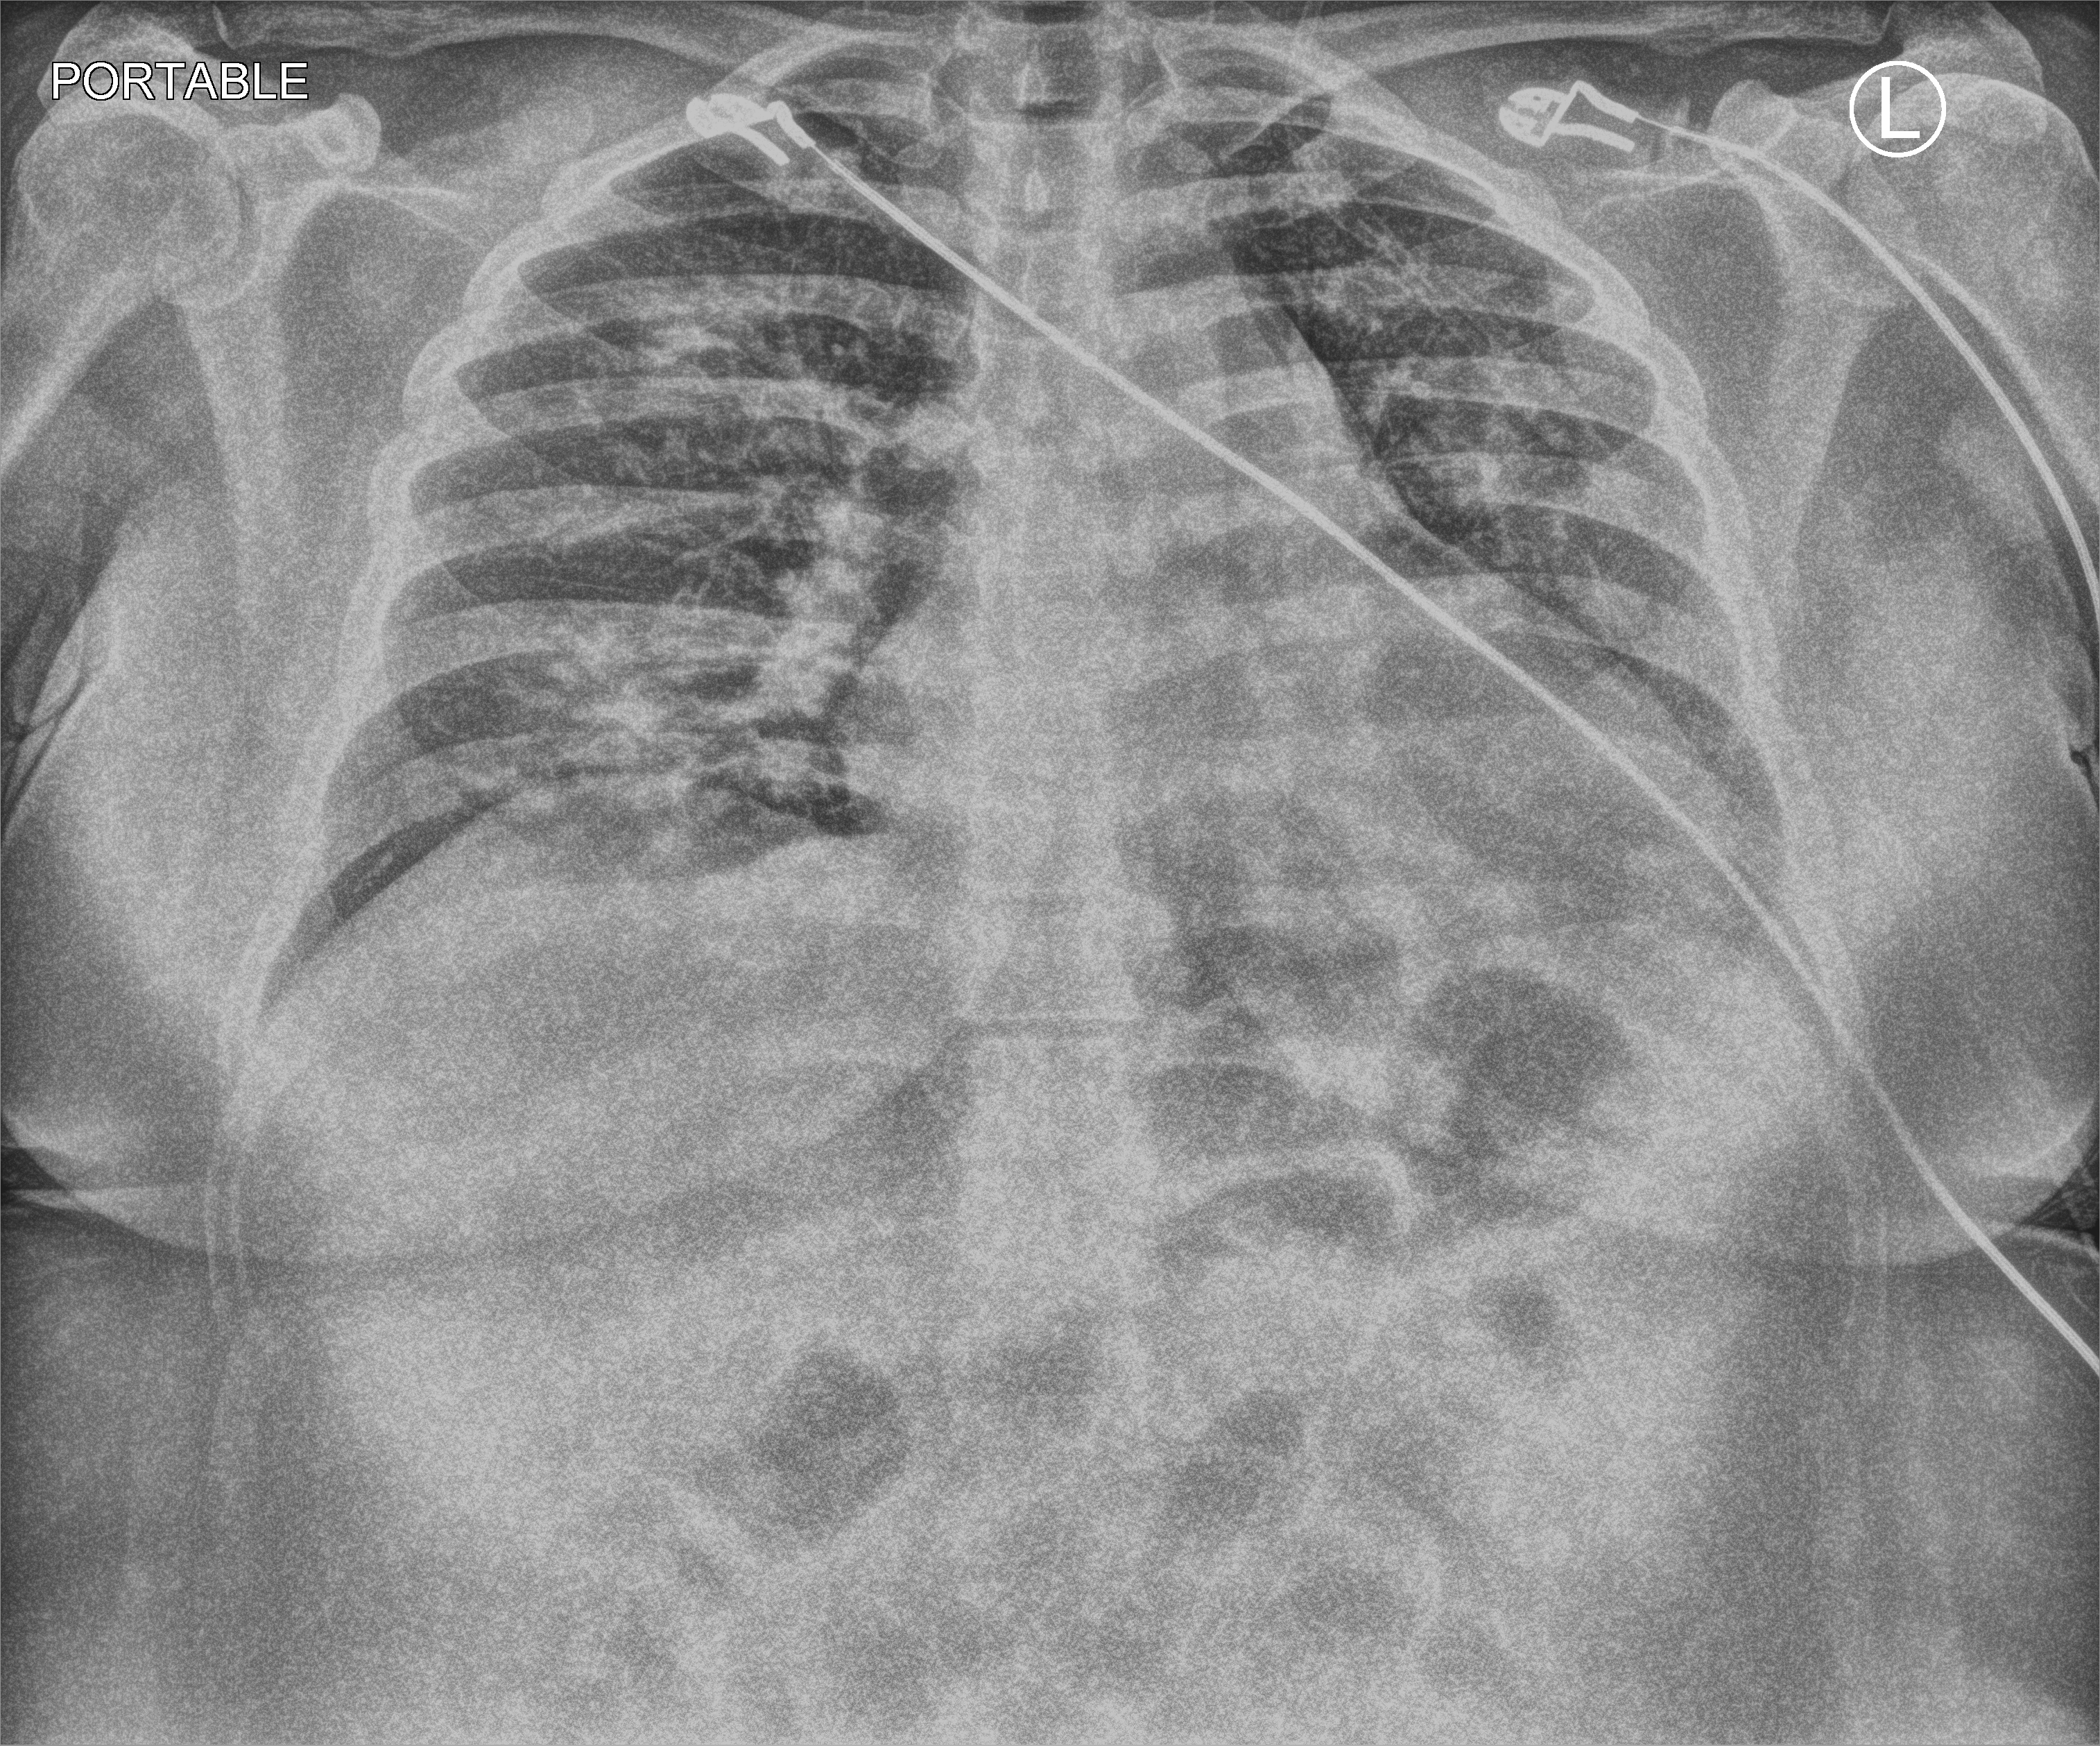
Portable chest radiograph. Patient hospitalised with COVID-19; female, aged 18–59 years.
From the hospital-stay record, not from the radiograph (when in the stay this image was taken is not recorded): mechanically ventilated during this hospital stay: no.